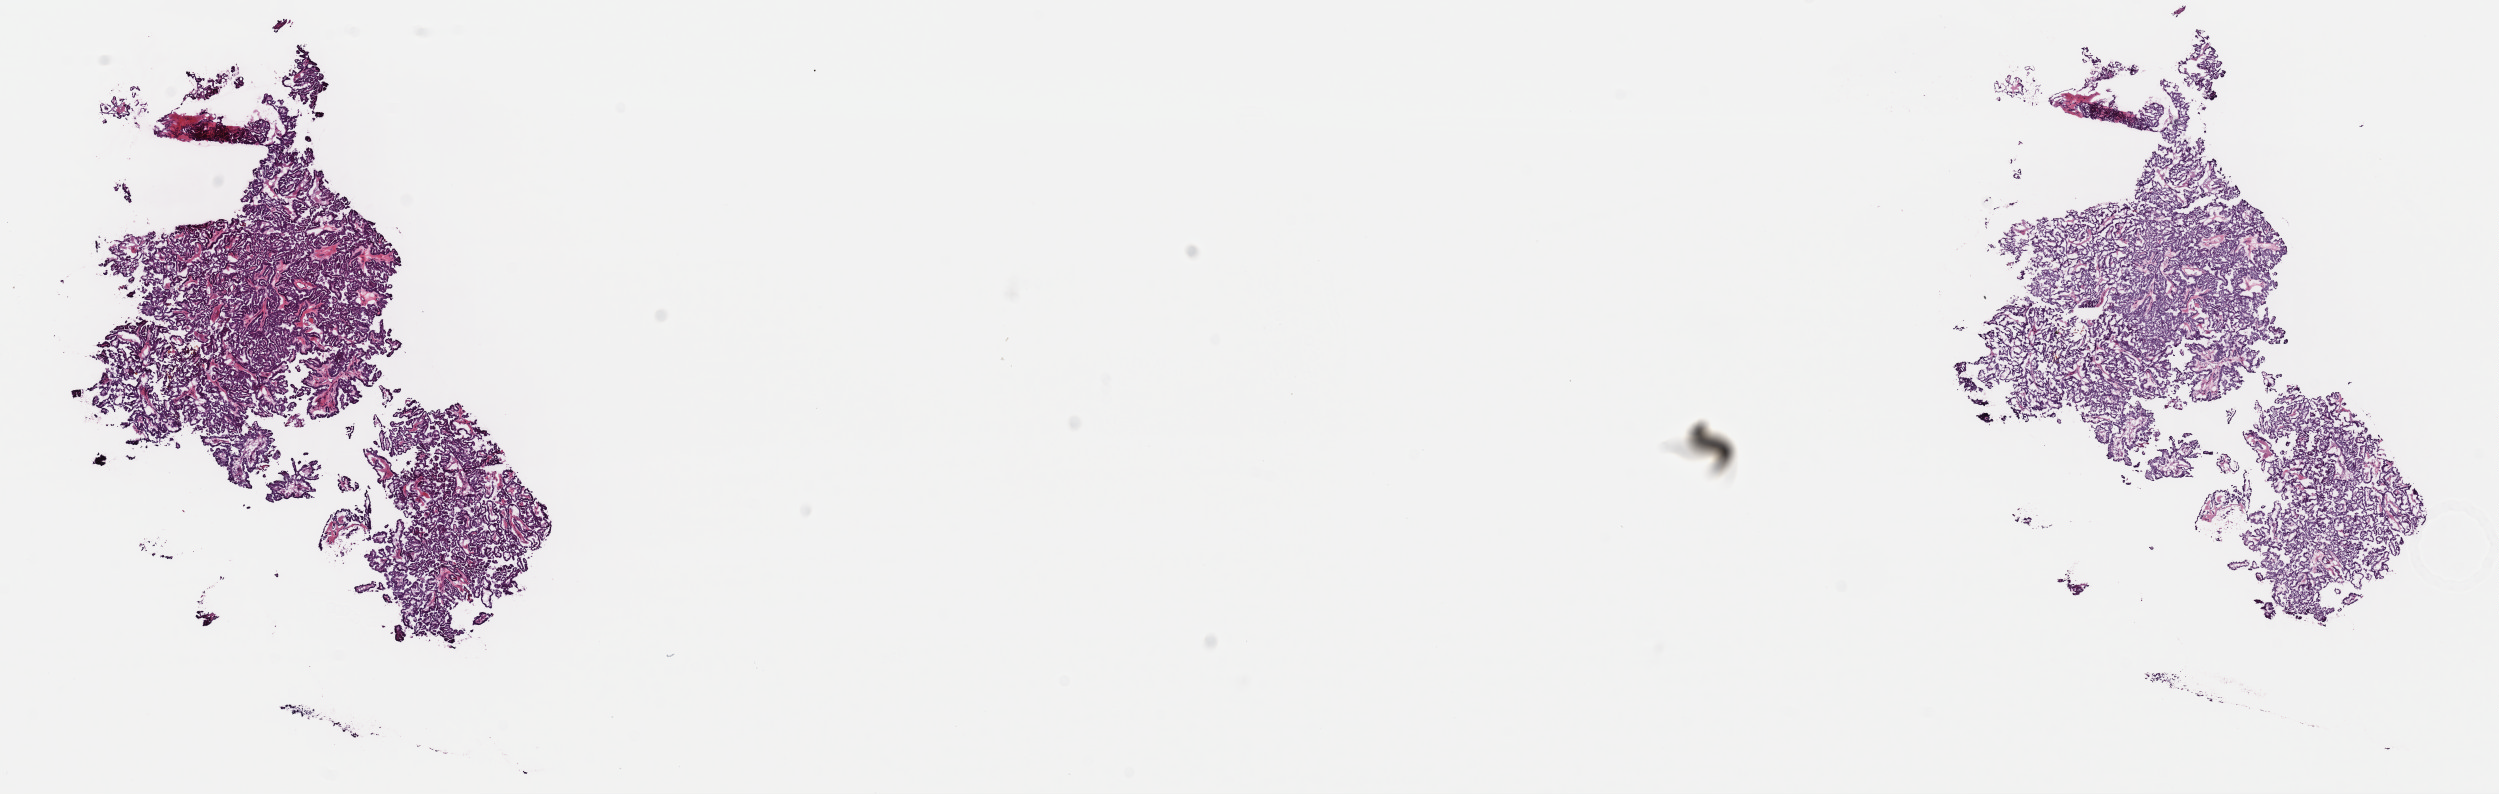
Whole-slide histology image, H&E-stained, low-resolution overview of the scanned area, about 19.7 x 6.3 mm (slide scanned at 40x). Frozen section. Primary tumour sample from the thyroid. Patient: male, age at initial diagnosis 27 years. Pathologist review of this section (percent, as recorded): tumour cells 80%, tumour nuclei 90%, normal cells 0%, stromal cells 20%, necrosis 0%. Infiltration values recorded for this section: lymphocyte infiltration 0%, monocyte infiltration 1%, neutrophil infiltration 0%.
Histologic diagnosis: Papillary adenocarcinoma, NOS. Lymph nodes positive (case pathology): 4 of 4 examined. AJCC pathologic stage: I (6th edition). Laterality: right.